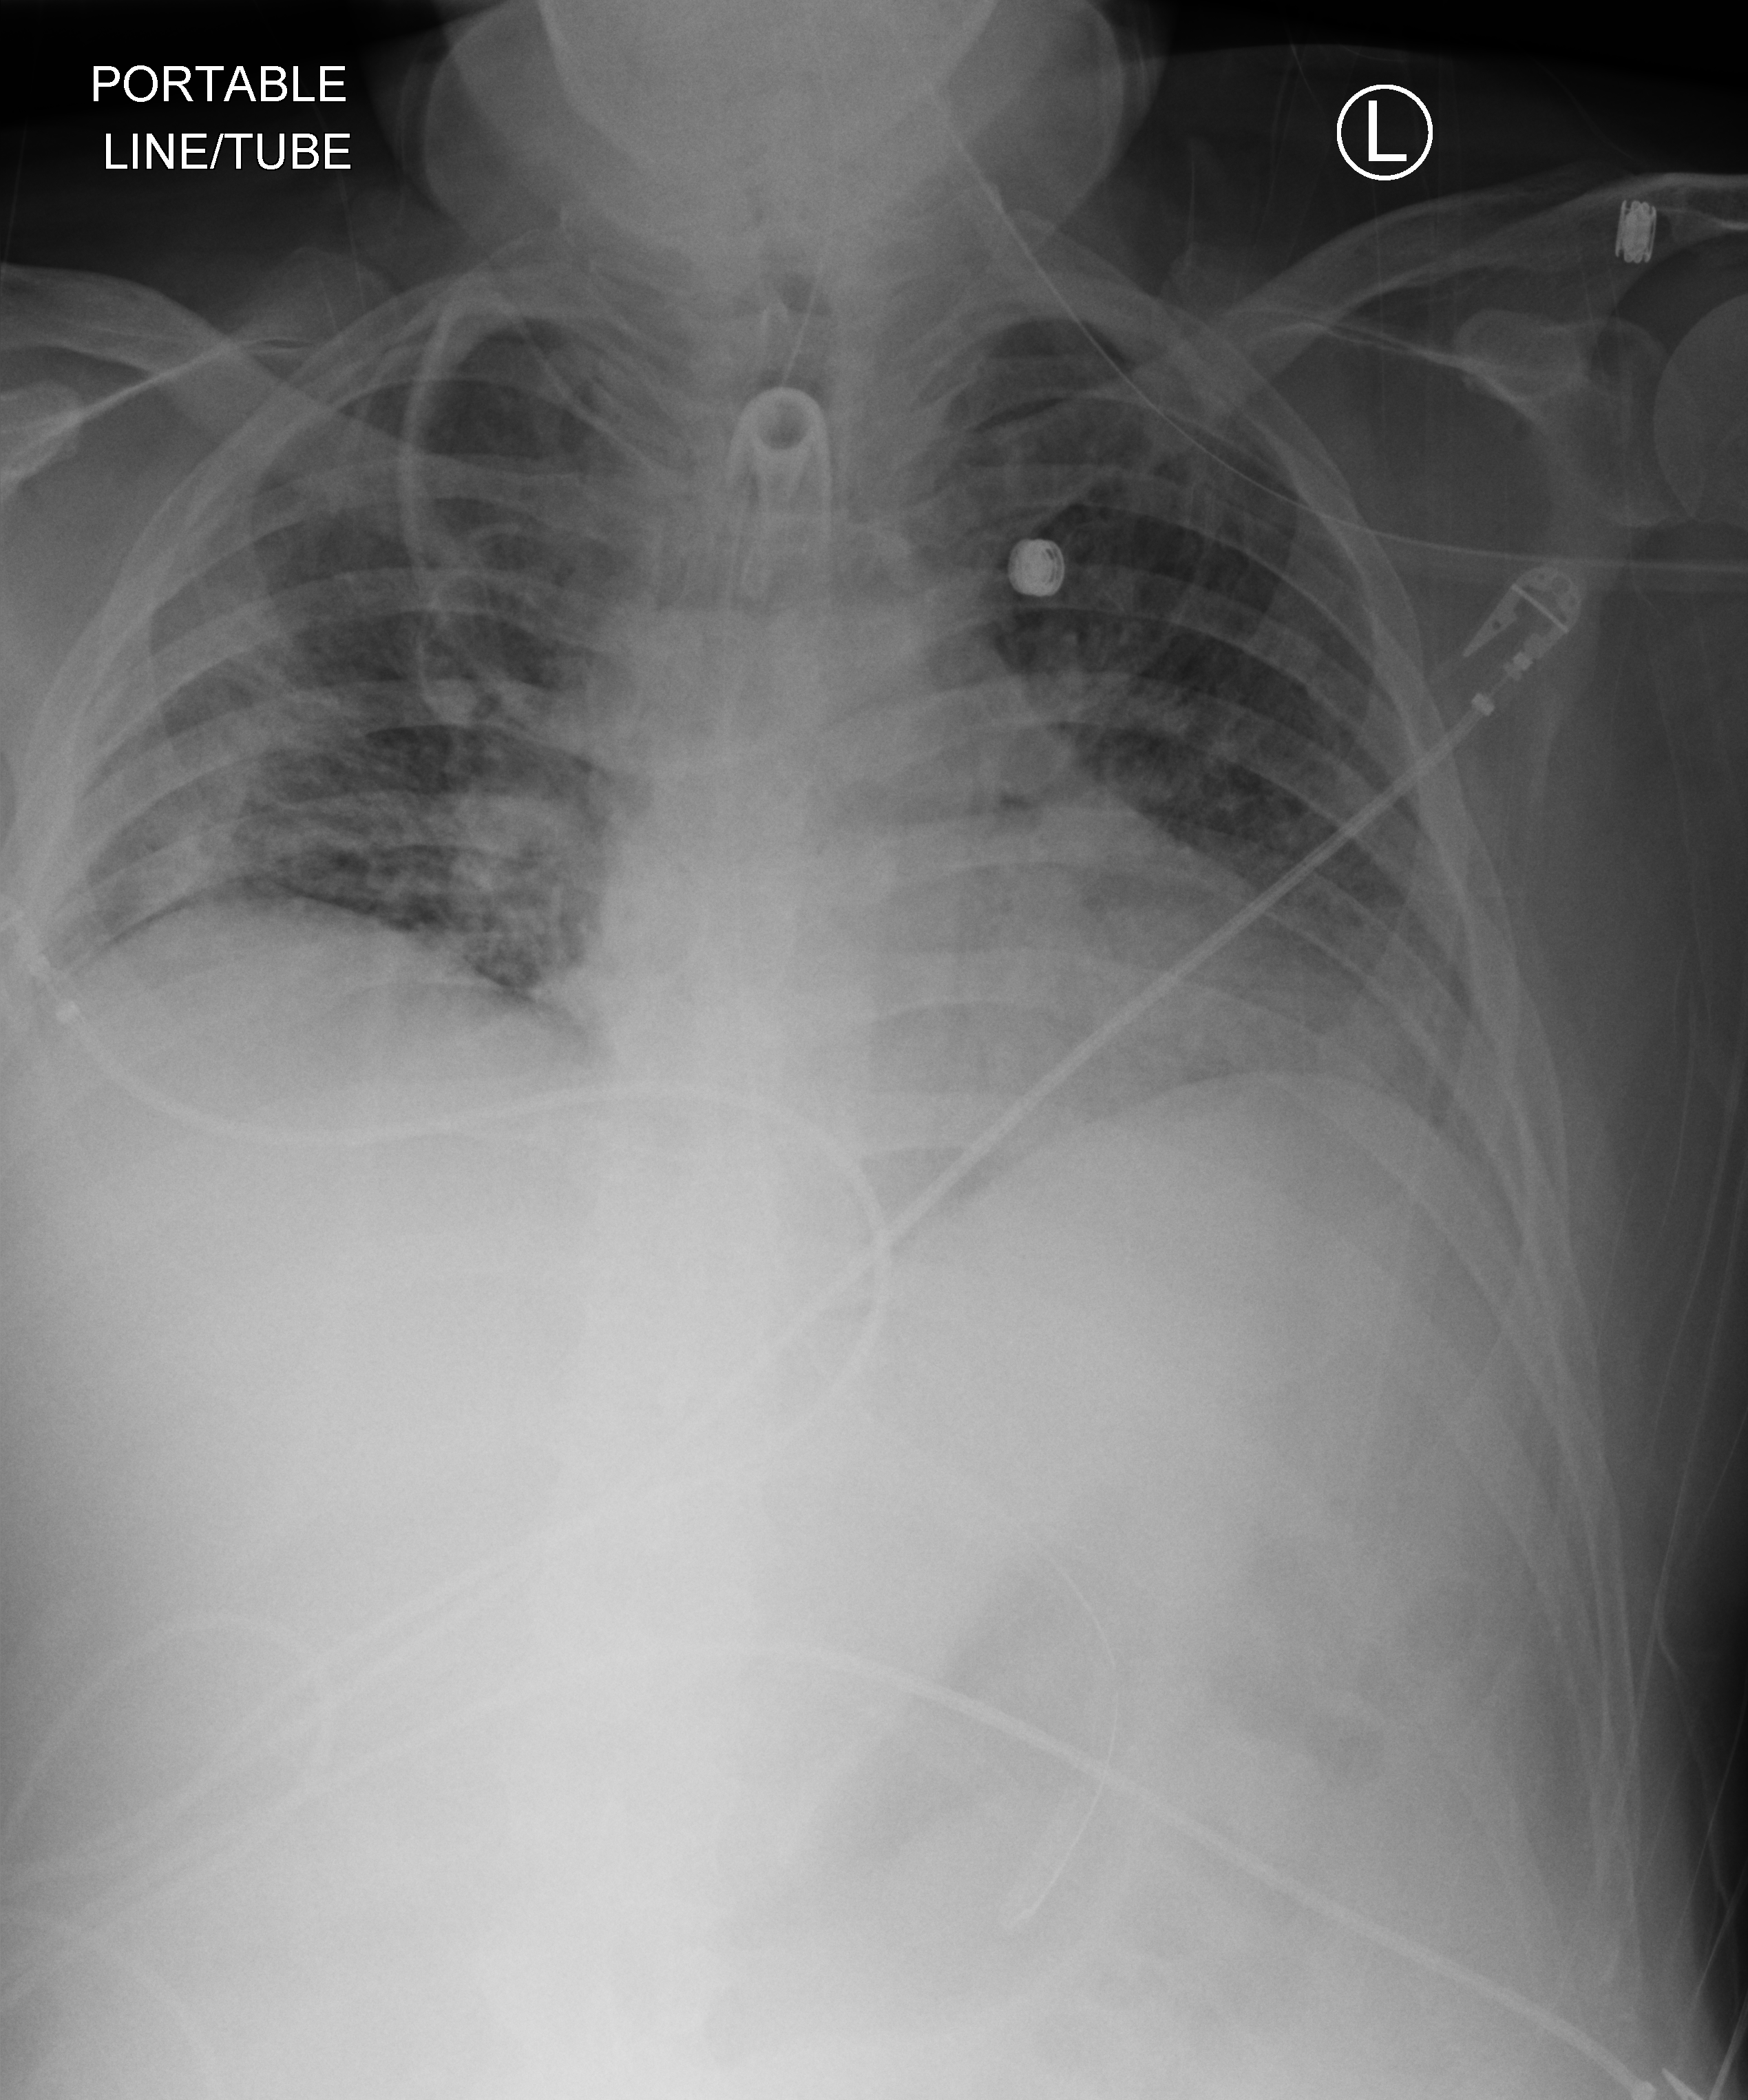
Portable chest radiograph, anteroposterior (AP) projection. Patient hospitalised with COVID-19; male, aged 18–59 years.
Admission-level facts for this patient (not findings on this image; timing relative to this image not recorded):
- smoking status (admission record): never